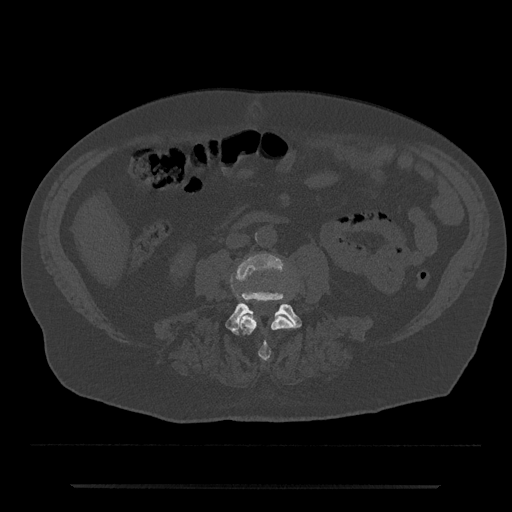
CT including the spine, one axial slice; 120 kVp; bone window (W 1800 / L 400 HU); 512 × 512 image matrix. Patient: male, 80 years. From the clinical record (not read from this slice): primary cancer: prostate.
Structures marked on this image (semi-automatic segmentation, software-assisted and operator-edited):
- L3 vertebra: bounding box (x1, y1, x2, y2) in pixels: (231, 254, 294, 361)
- L4 vertebra: (225, 291, 302, 335)